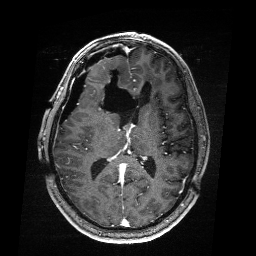
Brain MRI from a brain-tumour surgery series, one axial slice; position 97 of 176 along the scan axis; T1-weighted post-contrast; 256 × 256 image matrix. Case-level facts recorded for this patient, not image findings: histopathology: Astrocytoma; WHO grade: 4; IDH mutation: yes.
Annotated regions visible in this slice (manually delineated by an expert):
- residual tumour: box from (x=97, y=132) to (x=102, y=136) px